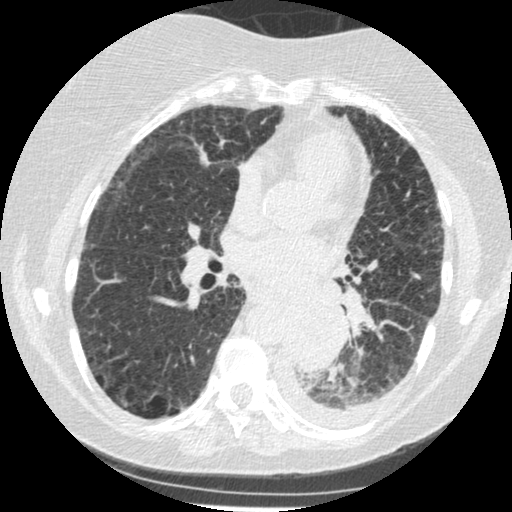
Axial slice from a low-dose chest CT screening exam. Third screening round (two years after baseline). Lung window (W 1500 / L -600 HU). Slice 223 of 341 in the series. Female, age 60 years at enrolment. Former smoker at enrolment.
Expert reader's lesion annotation, box from (x=274, y=305) to (x=343, y=375) px. The exam's reader record, not a measurement of the box and not confirmed to be the same lesion: non-calcified nodule or mass ≥4 mm, left lower lobe, 54 × 38 mm, smooth margins, soft tissue attenuation, pre-existing on the prior screen: yes; interval growth: yes. Official screen result: positive, other. Participant outcome: lung cancer diagnosed 15 days after this screen — small cell carcinoma, NOS, left lower lobe, undifferentiated (G4), stage IV (AJCC 6th edition), 69 mm at pathology.